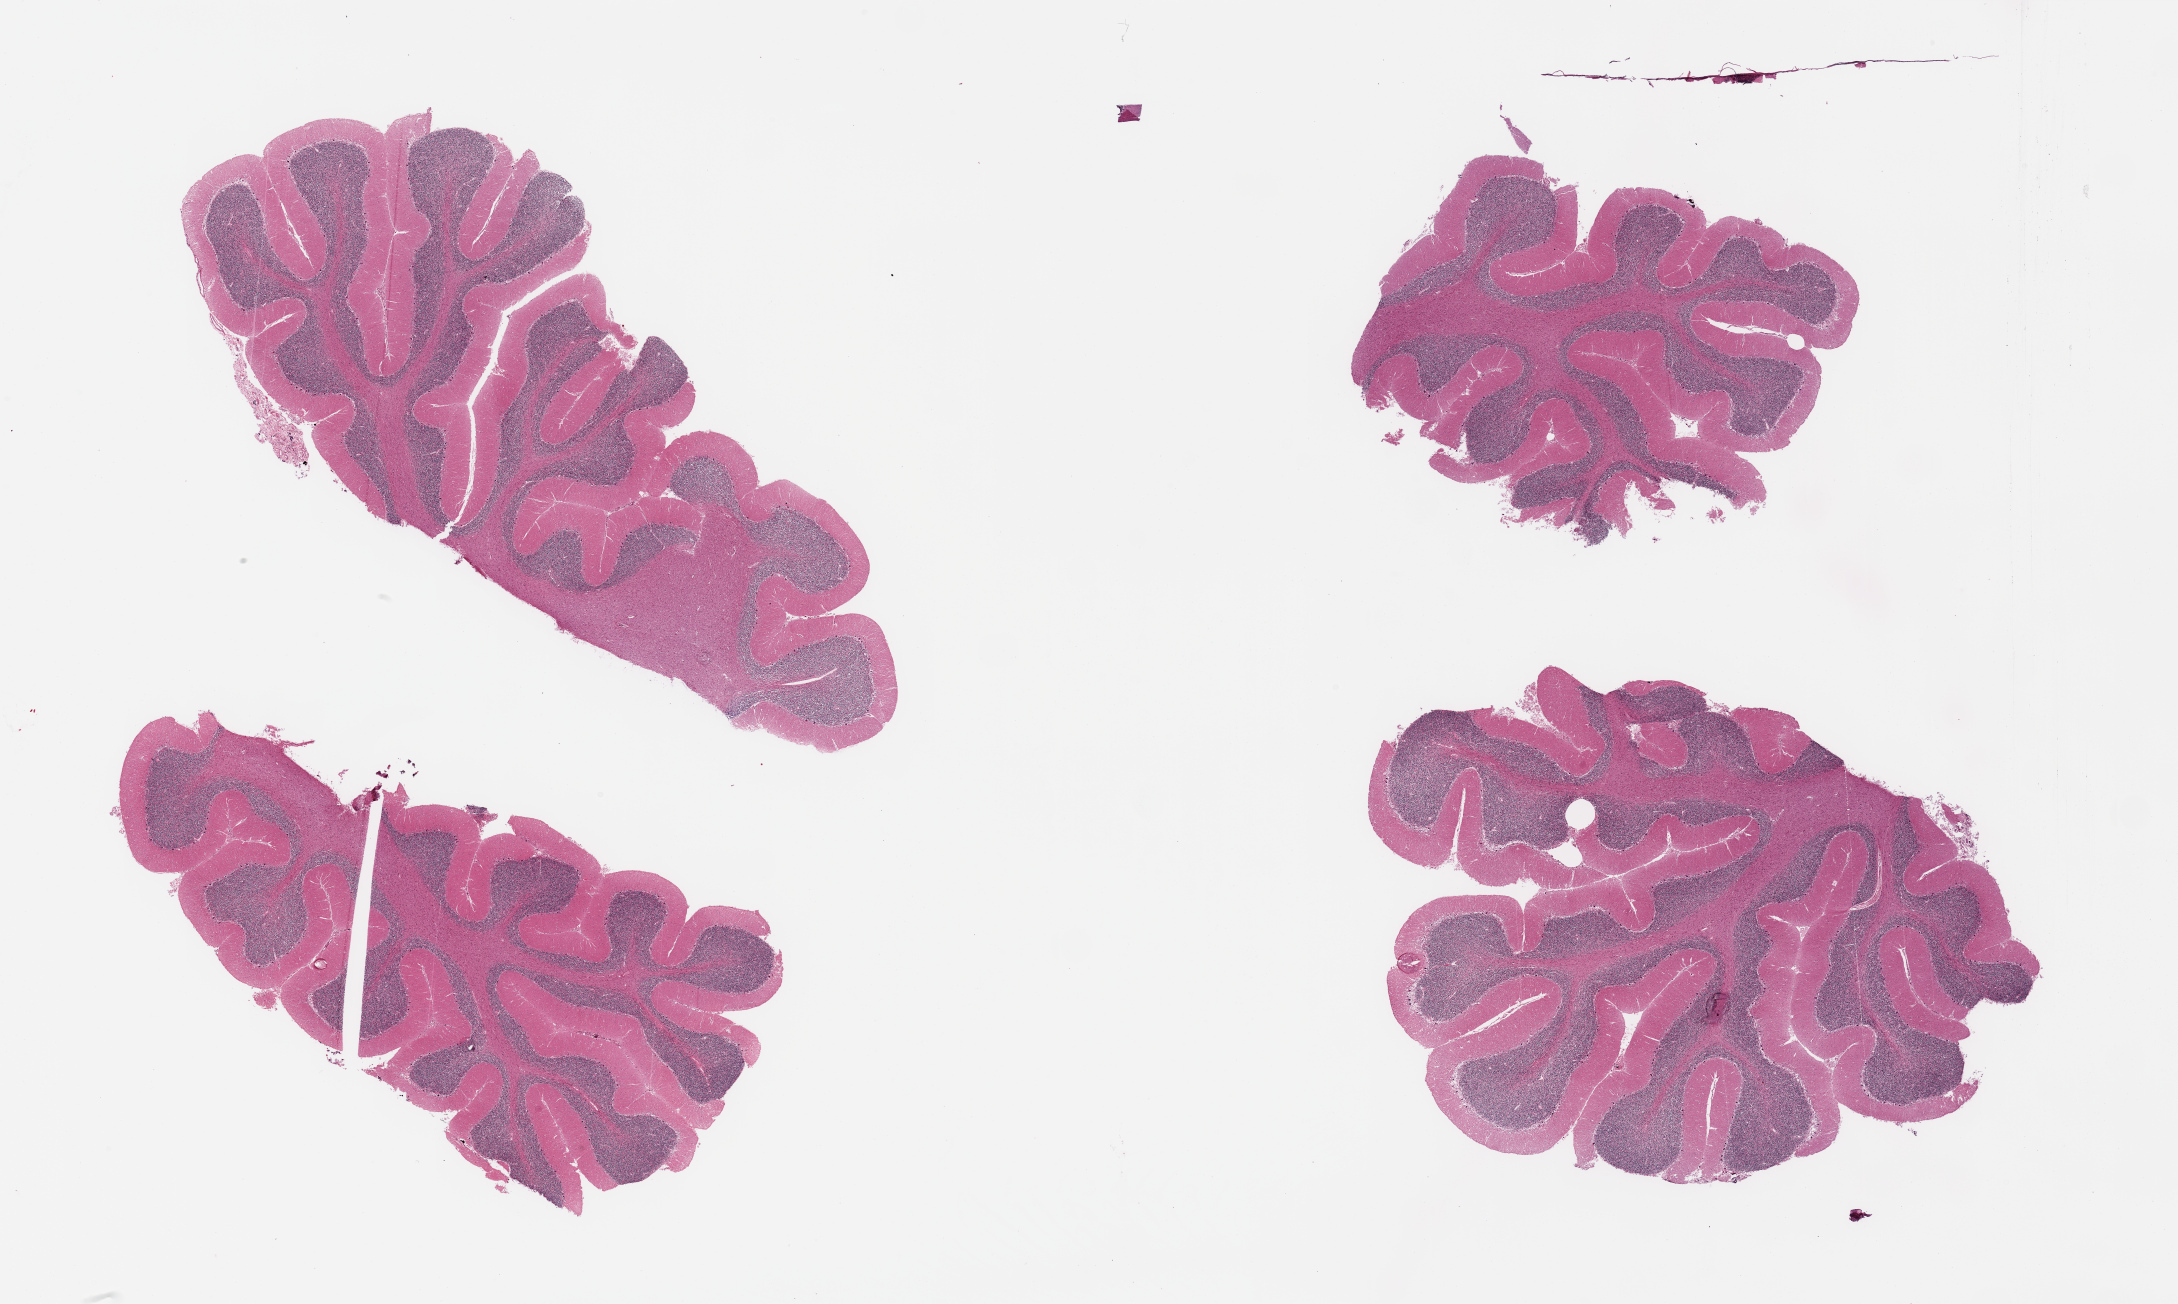
Hematoxylin and eosin (H&E) whole-slide image, whole scanned area (about 34.5 x 20.6 mm) shown as a low-resolution overview. PAXgene-fixed, paraffin-embedded tissue. Target tissue: cerebellum. Tissue donor sample. Donor sex: male.
Pathologist's review note for this sample: 4 pieces, no abnormalities.